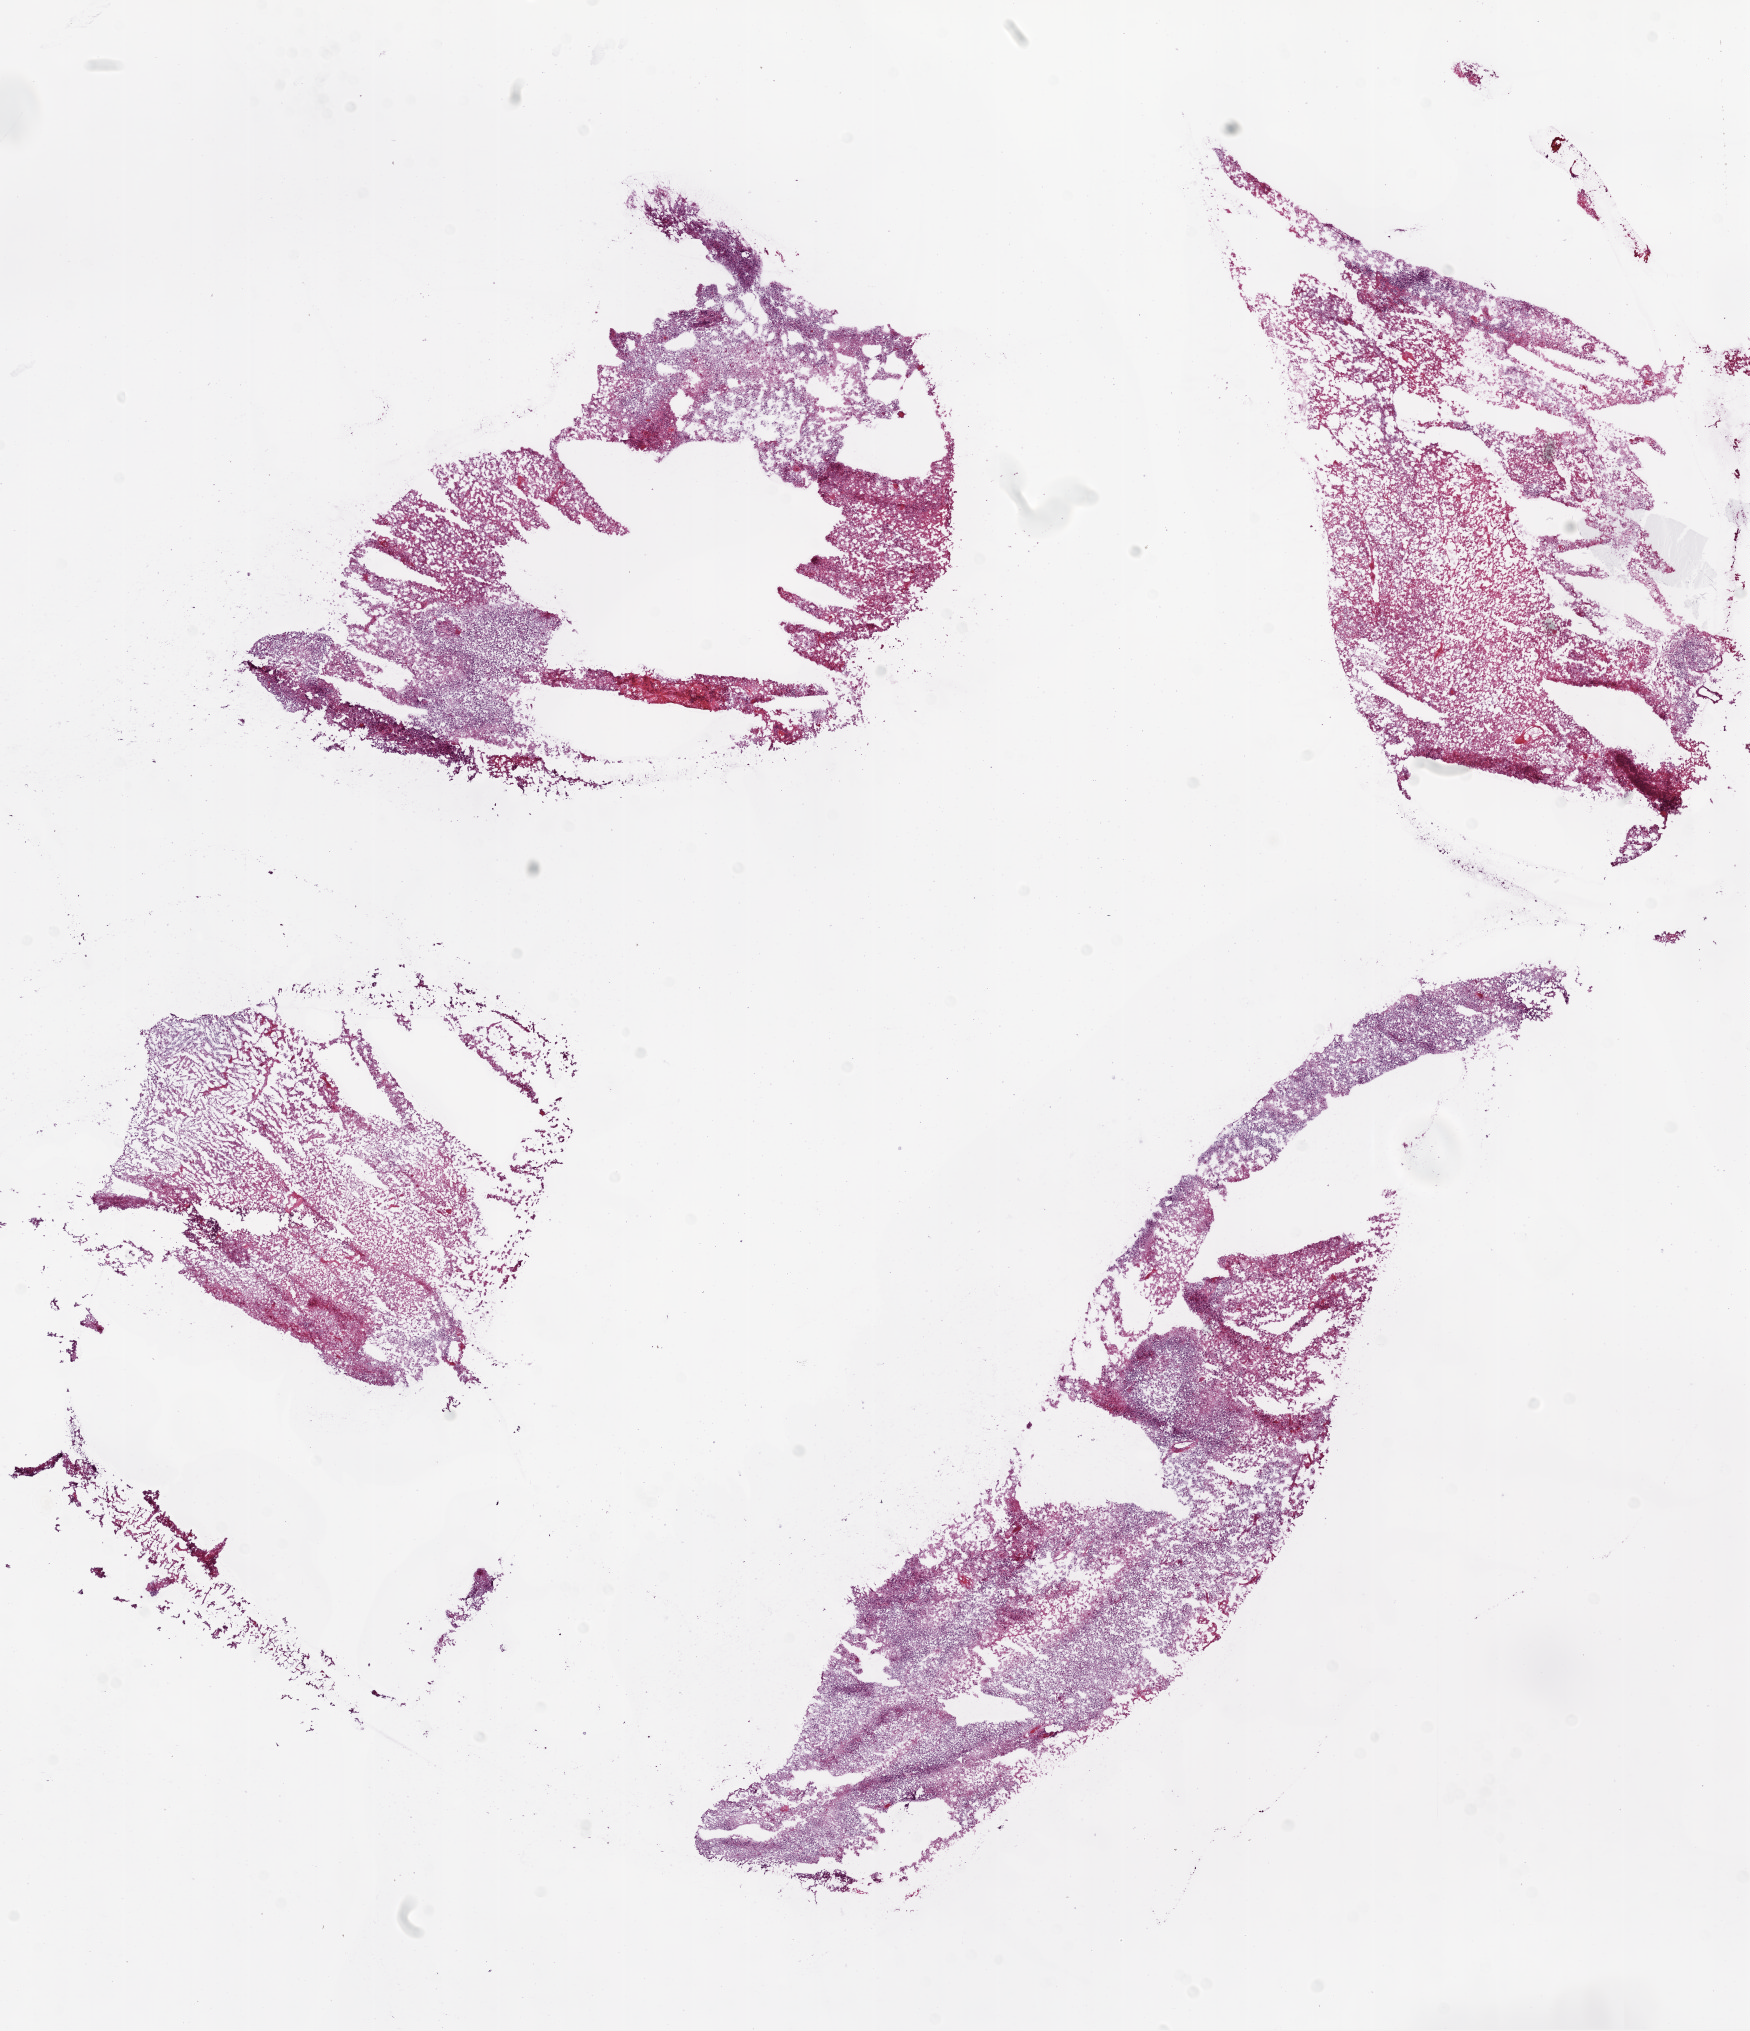
H&E whole-slide image, a low-resolution overview of the entire scanned area, about 14.0 x 16.3 mm; frozen section from the bottom of the tissue portion; sample: primary tumour, brain. Male, age 66 years at initial diagnosis. Composition of this section per pathologist review: tumour cells 50%, tumour nuclei 100%, normal cells 0%, stromal cells 0%, necrosis 50%.
- pathologic diagnosis: Glioblastoma